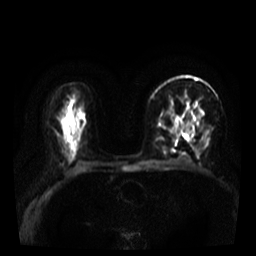
Breast MRI, one axial slice; position 22 of 39 along the scan axis; diffusion-weighted series; image 2 of 4 stored at this slice position (different b-values; order by instance number); 3 T; 5 mm slice thickness; 256 × 256 image matrix, field of view 320 × 320 mm. Female patient.
Structures marked on this image (outlined manually by an expert reader):
- tumour on diffusion-weighted imaging: bounding box [x1, y1, x2, y2] px = [181, 126, 185, 134]